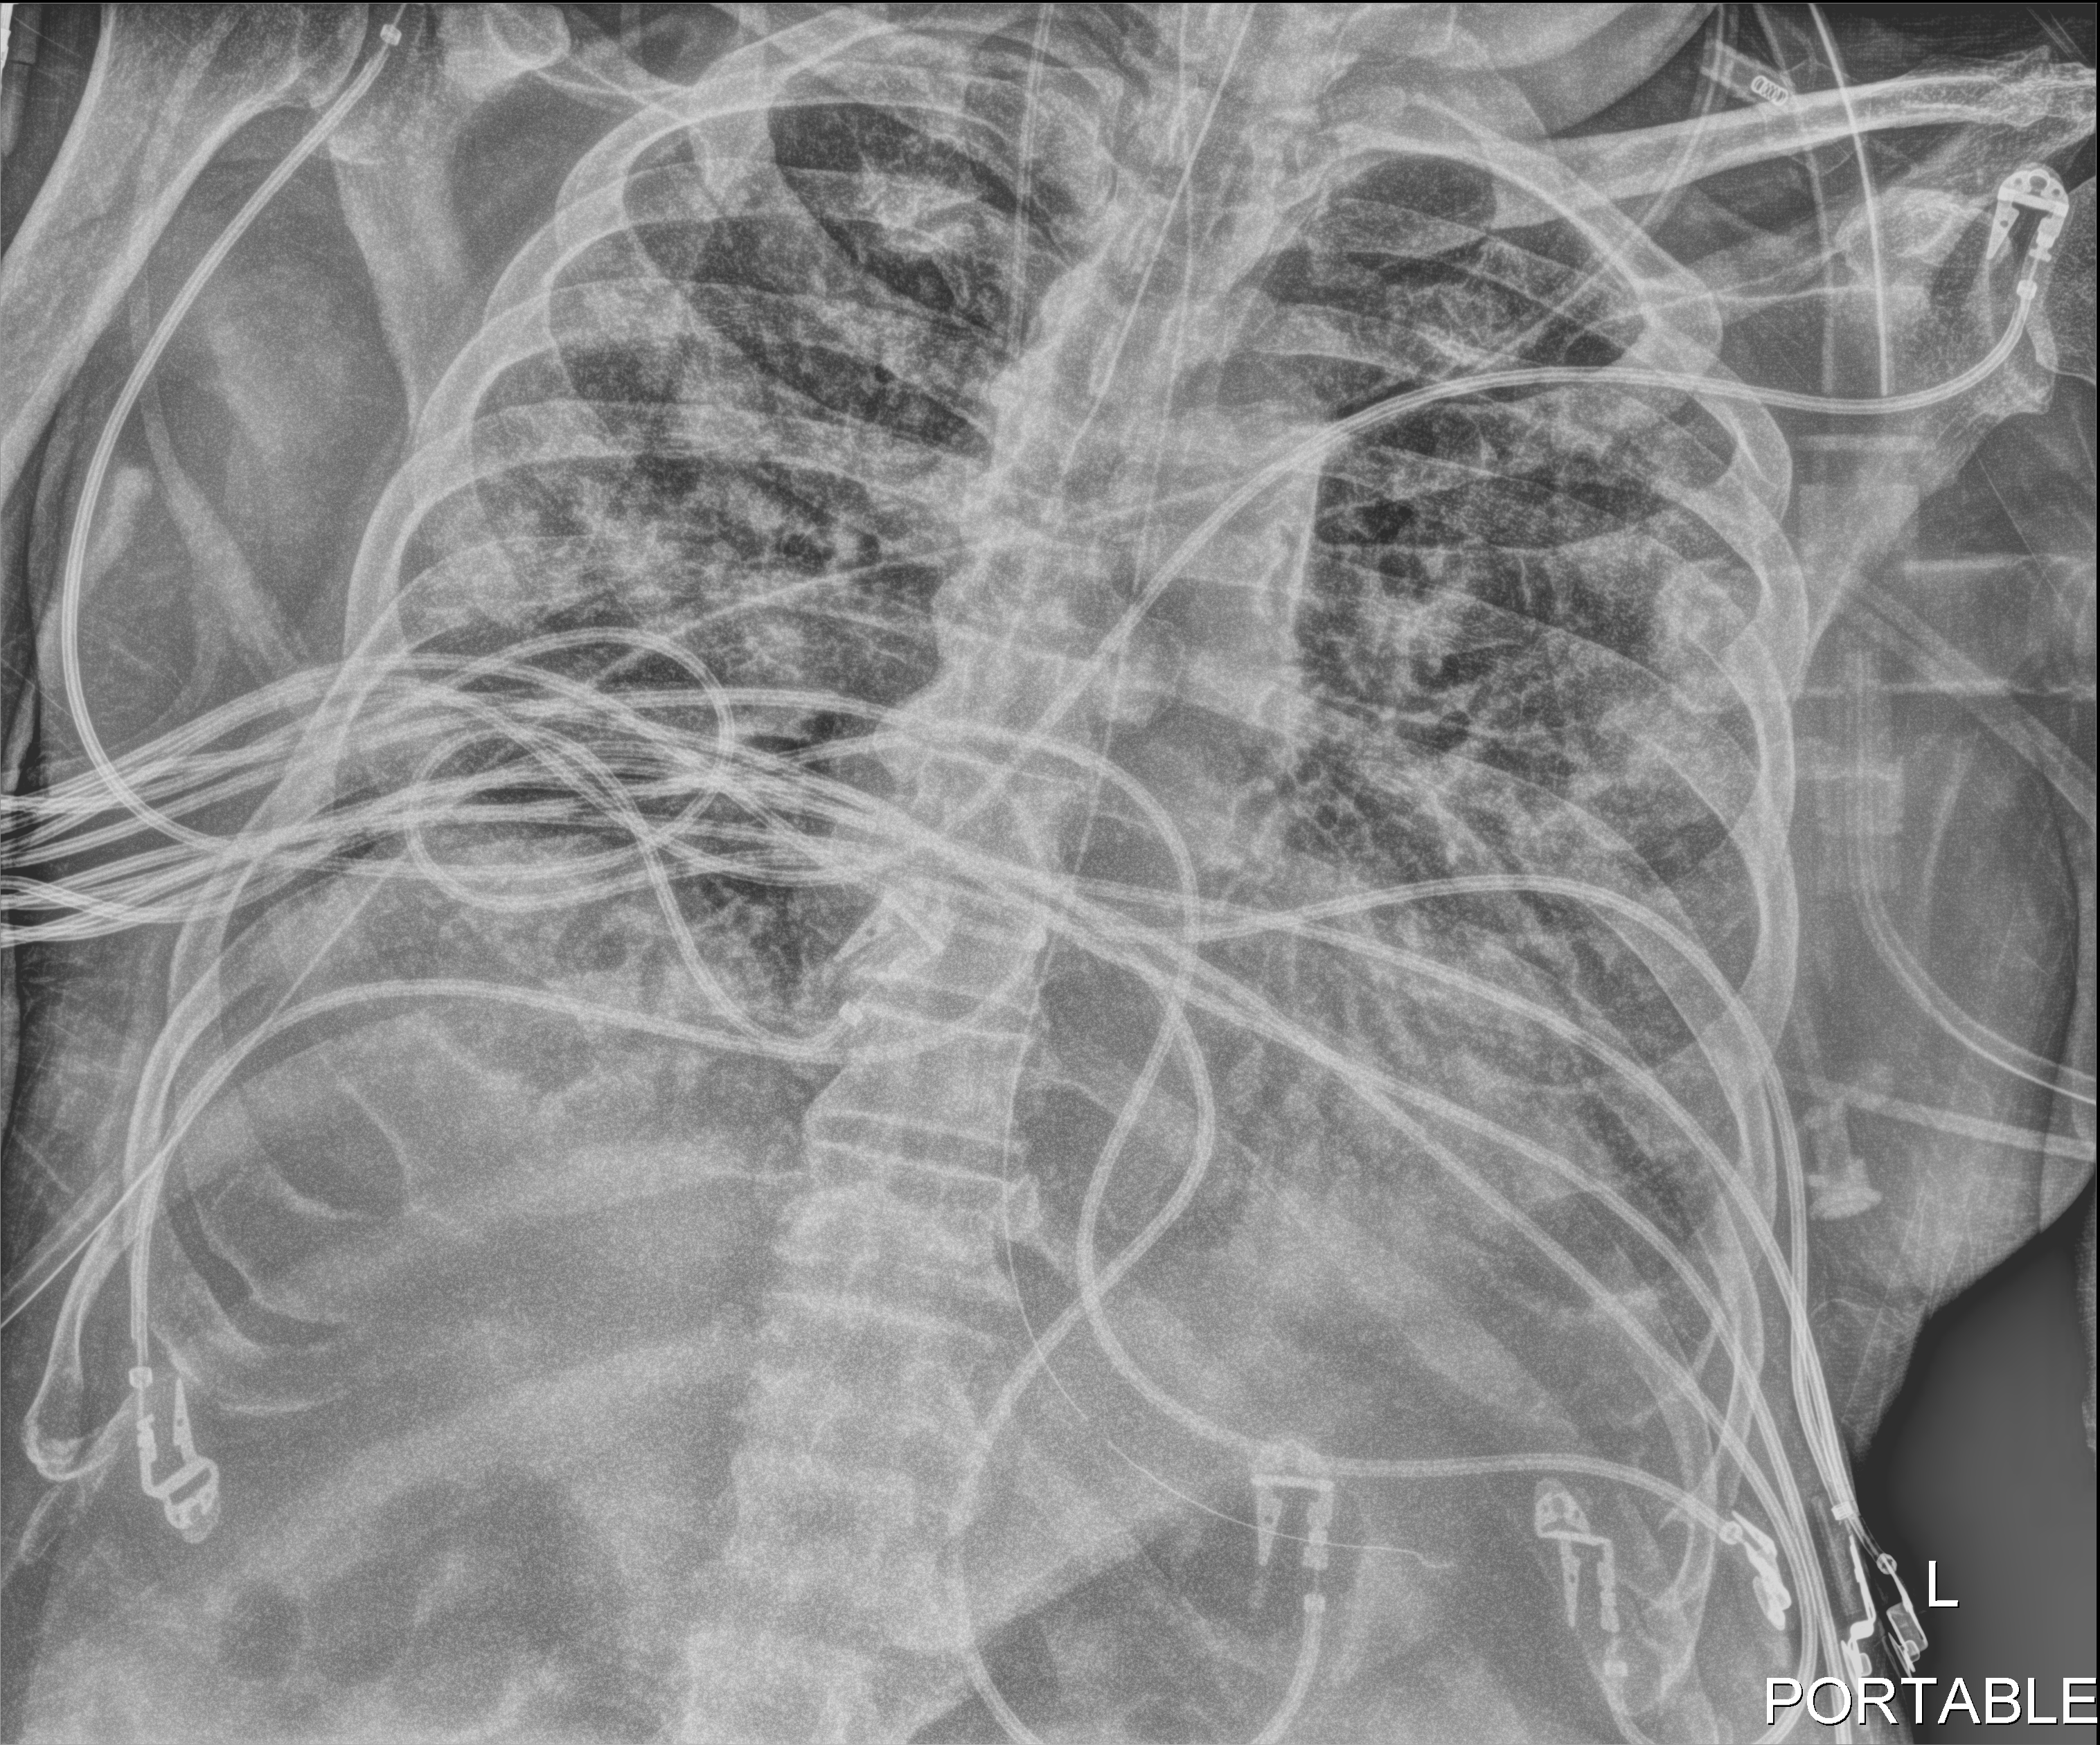
Chest X-ray (portable); anteroposterior (AP) projection. Male patient hospitalised with COVID-19, age 75–90 years.
Hospital-stay facts (about this admission, not read from this image; timing relative to this image not recorded): chronic kidney disease (admission record): no; diabetes (admission record): no; other chronic lung disease (admission record): no.